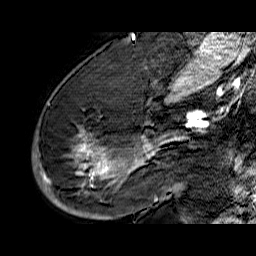
Breast MRI (dynamic contrast-enhanced), one sagittal slice; slice 39 of 60 in the series (ordered by position); dynamic contrast-enhanced series, time point 2 of 6 at this slice position (early post-contrast); 1.5 T; TE 6.5 ms, TR 32.9 ms; 4 mm slice thickness; 256 × 256 image matrix, field of view 200 × 200 mm. Female patient. From the clinical record (not read from this slice): setting: breast cancer imaged before/during neoadjuvant chemotherapy; receptor status: HR-positive, HER2-negative.
Annotated regions visible in this slice (semi-automatic segmentation, software-assisted and operator-edited):
- analysis volume of interest (the breast-tissue region the enhancement analysis was run in; not a lesion): bounding box (x1, y1, x2, y2) in pixels: (33, 74, 176, 210)
- tumour enhancement mask (voxels above the 100 % enhancement threshold inside the analysis volume of interest): (39, 133, 176, 193)